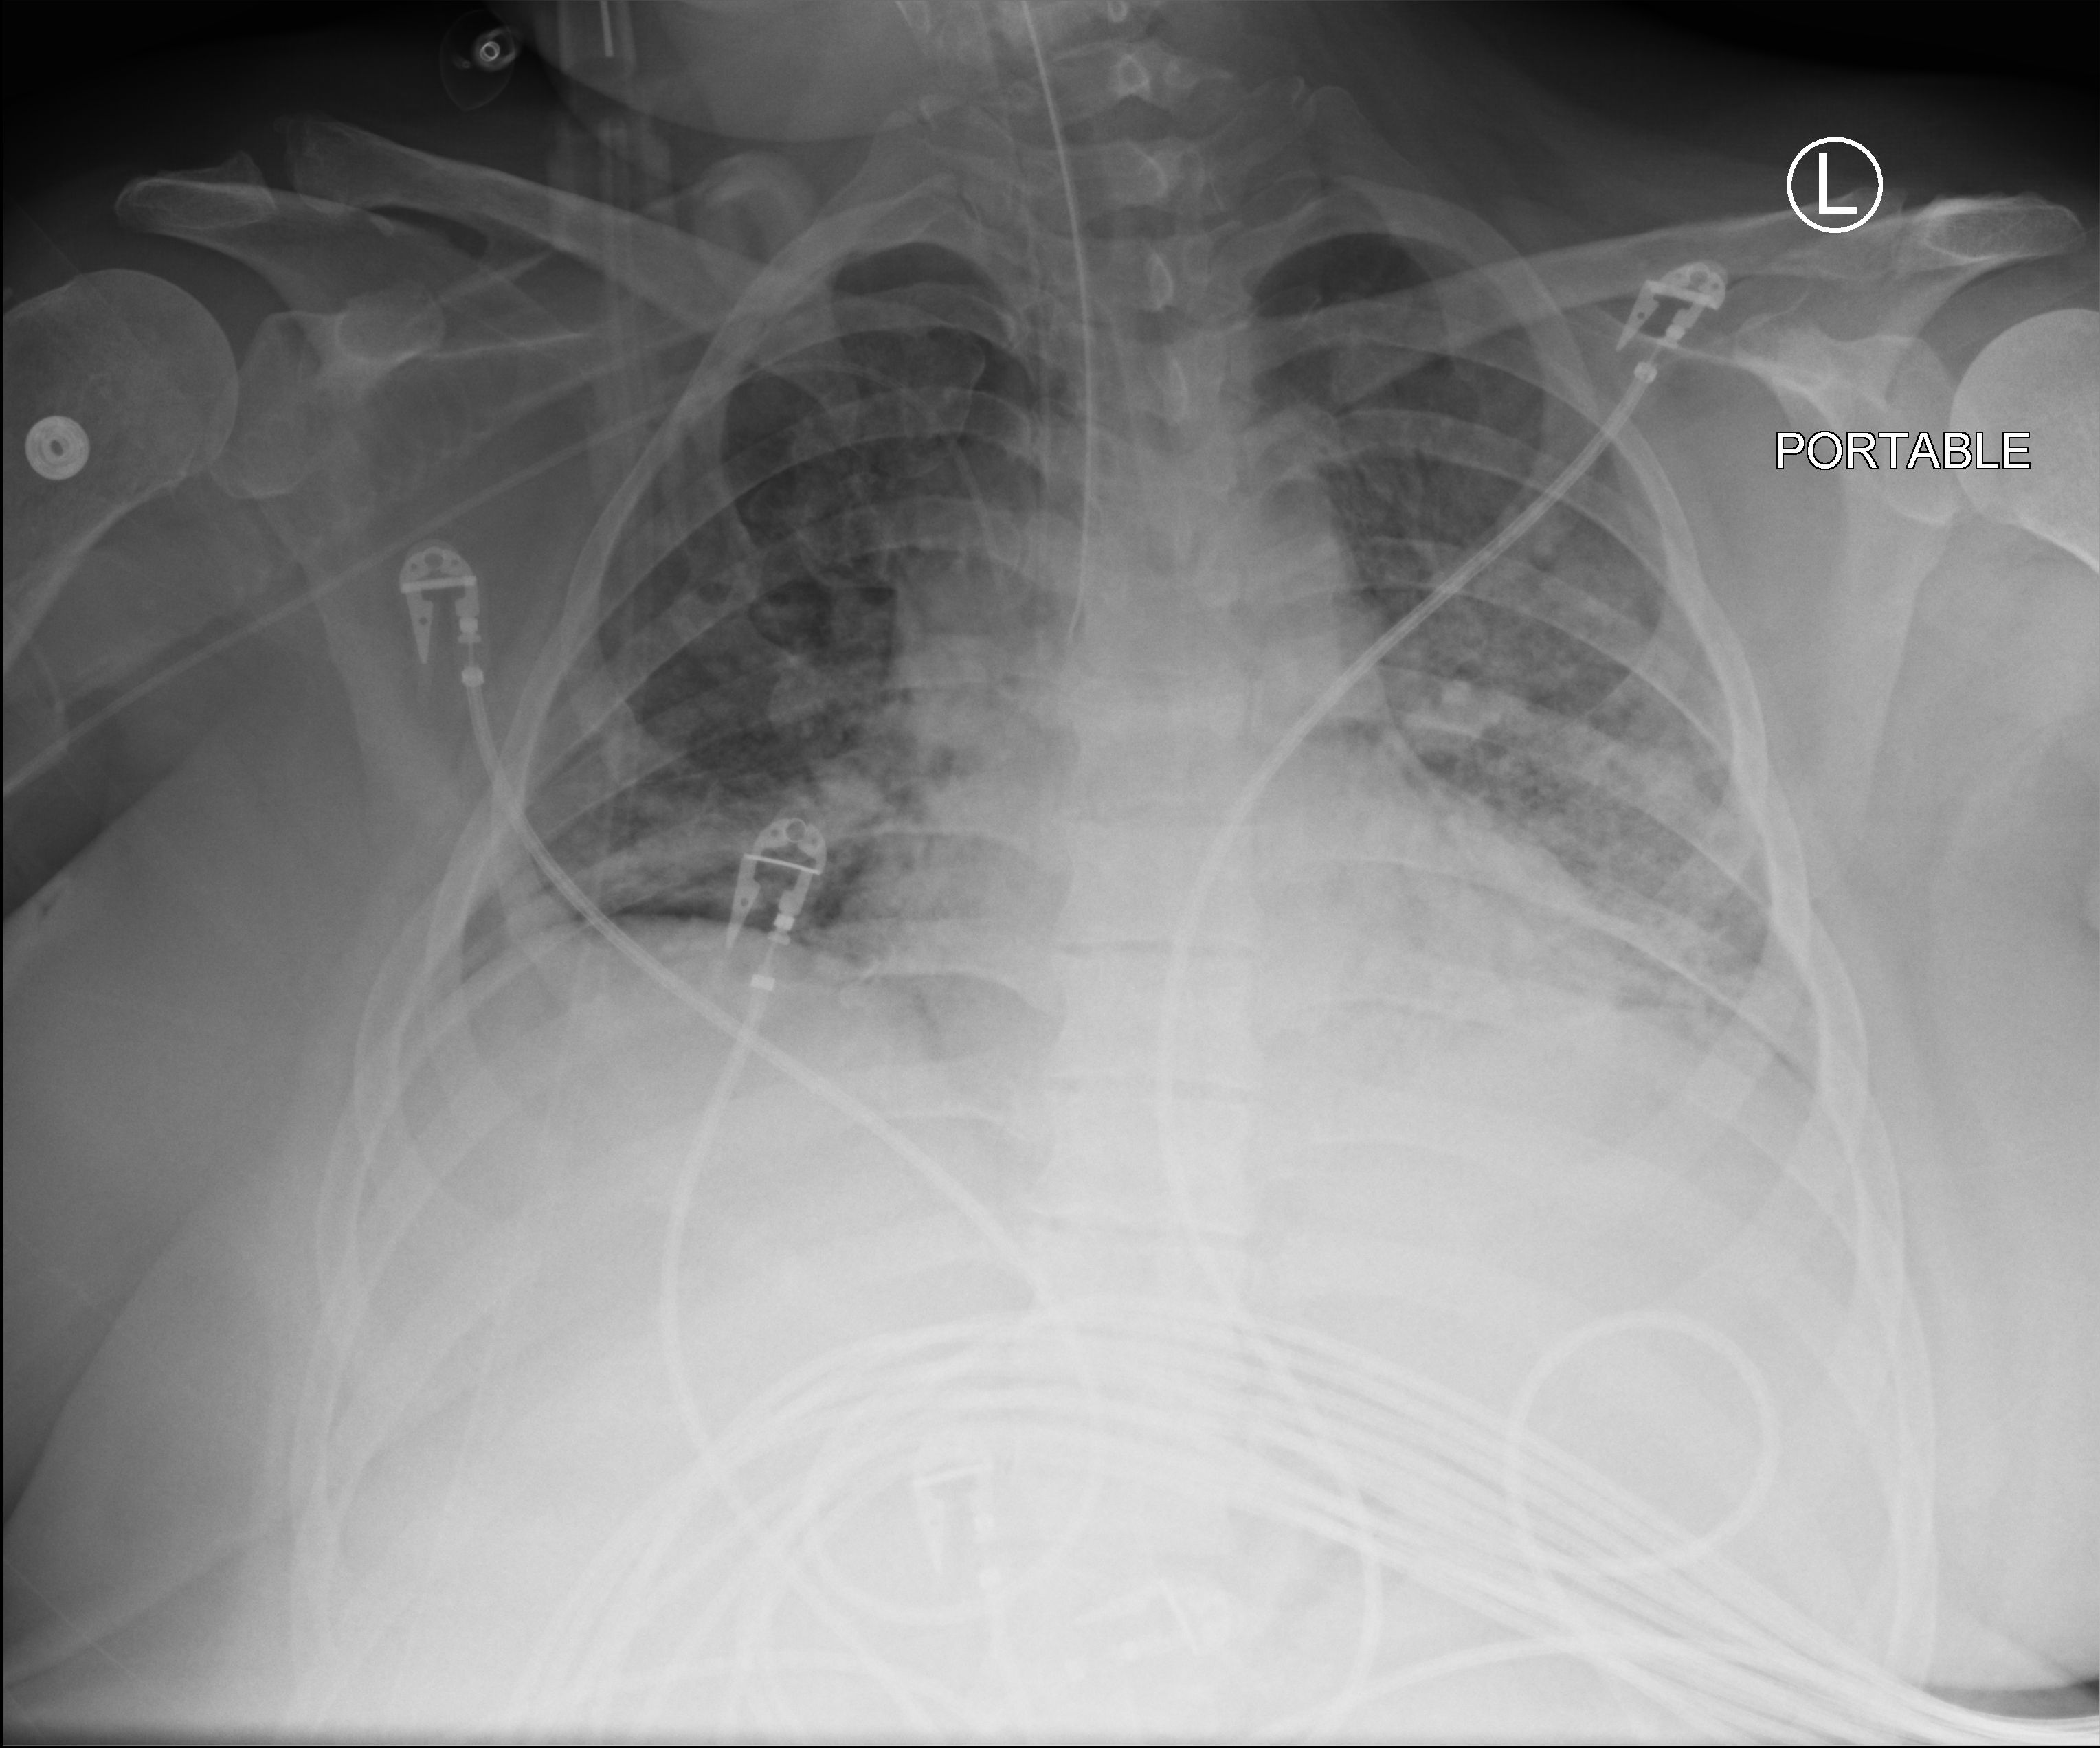
Portable chest radiograph; anteroposterior (AP) projection. Patient hospitalised with COVID-19; female, aged 18–59 years.
Hospital-stay facts (about this admission, not read from this image; timing relative to this image not recorded): mechanically ventilated during this hospital stay: yes; length of hospital stay: 25 days; other chronic lung disease (admission record): no.